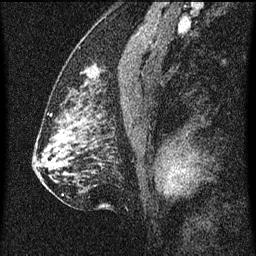
Breast MRI (dynamic contrast-enhanced), one sagittal slice; position 35 of 60 along the scan axis; dynamic contrast-enhanced series, image 2 of 3 at this slice position (ordered by acquisition); 1.5 T; TE 4.2 ms, TR 8 ms; 256 × 256 image matrix. Female patient, age 52 years.
Structures marked on this image (semi-automatic segmentation, software-assisted and operator-edited):
- analysis volume of interest (the breast-tissue region the enhancement analysis was run in; not a lesion): box from (x=72, y=50) to (x=115, y=101) px
- tumour enhancement mask (voxels above the 70 % enhancement threshold inside the analysis volume of interest): (x=85, y=70)–(x=90, y=85)